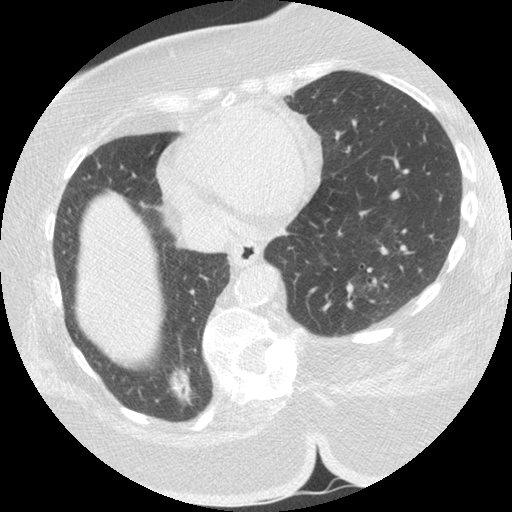
Low-dose screening chest CT, one axial slice. Slice 51 of 151 in the series (ordered by position). 140 kVp. Lung window (W 1500 / L -600 HU). 512 × 512 image matrix, field of view 340 × 340 mm.
Annotated regions visible in this slice (manually delineated by an expert):
- lesion 1 (tumor, lower lobe of right lung): bounding box (x1, y1, x2, y2) in pixels: (171, 366, 194, 403)